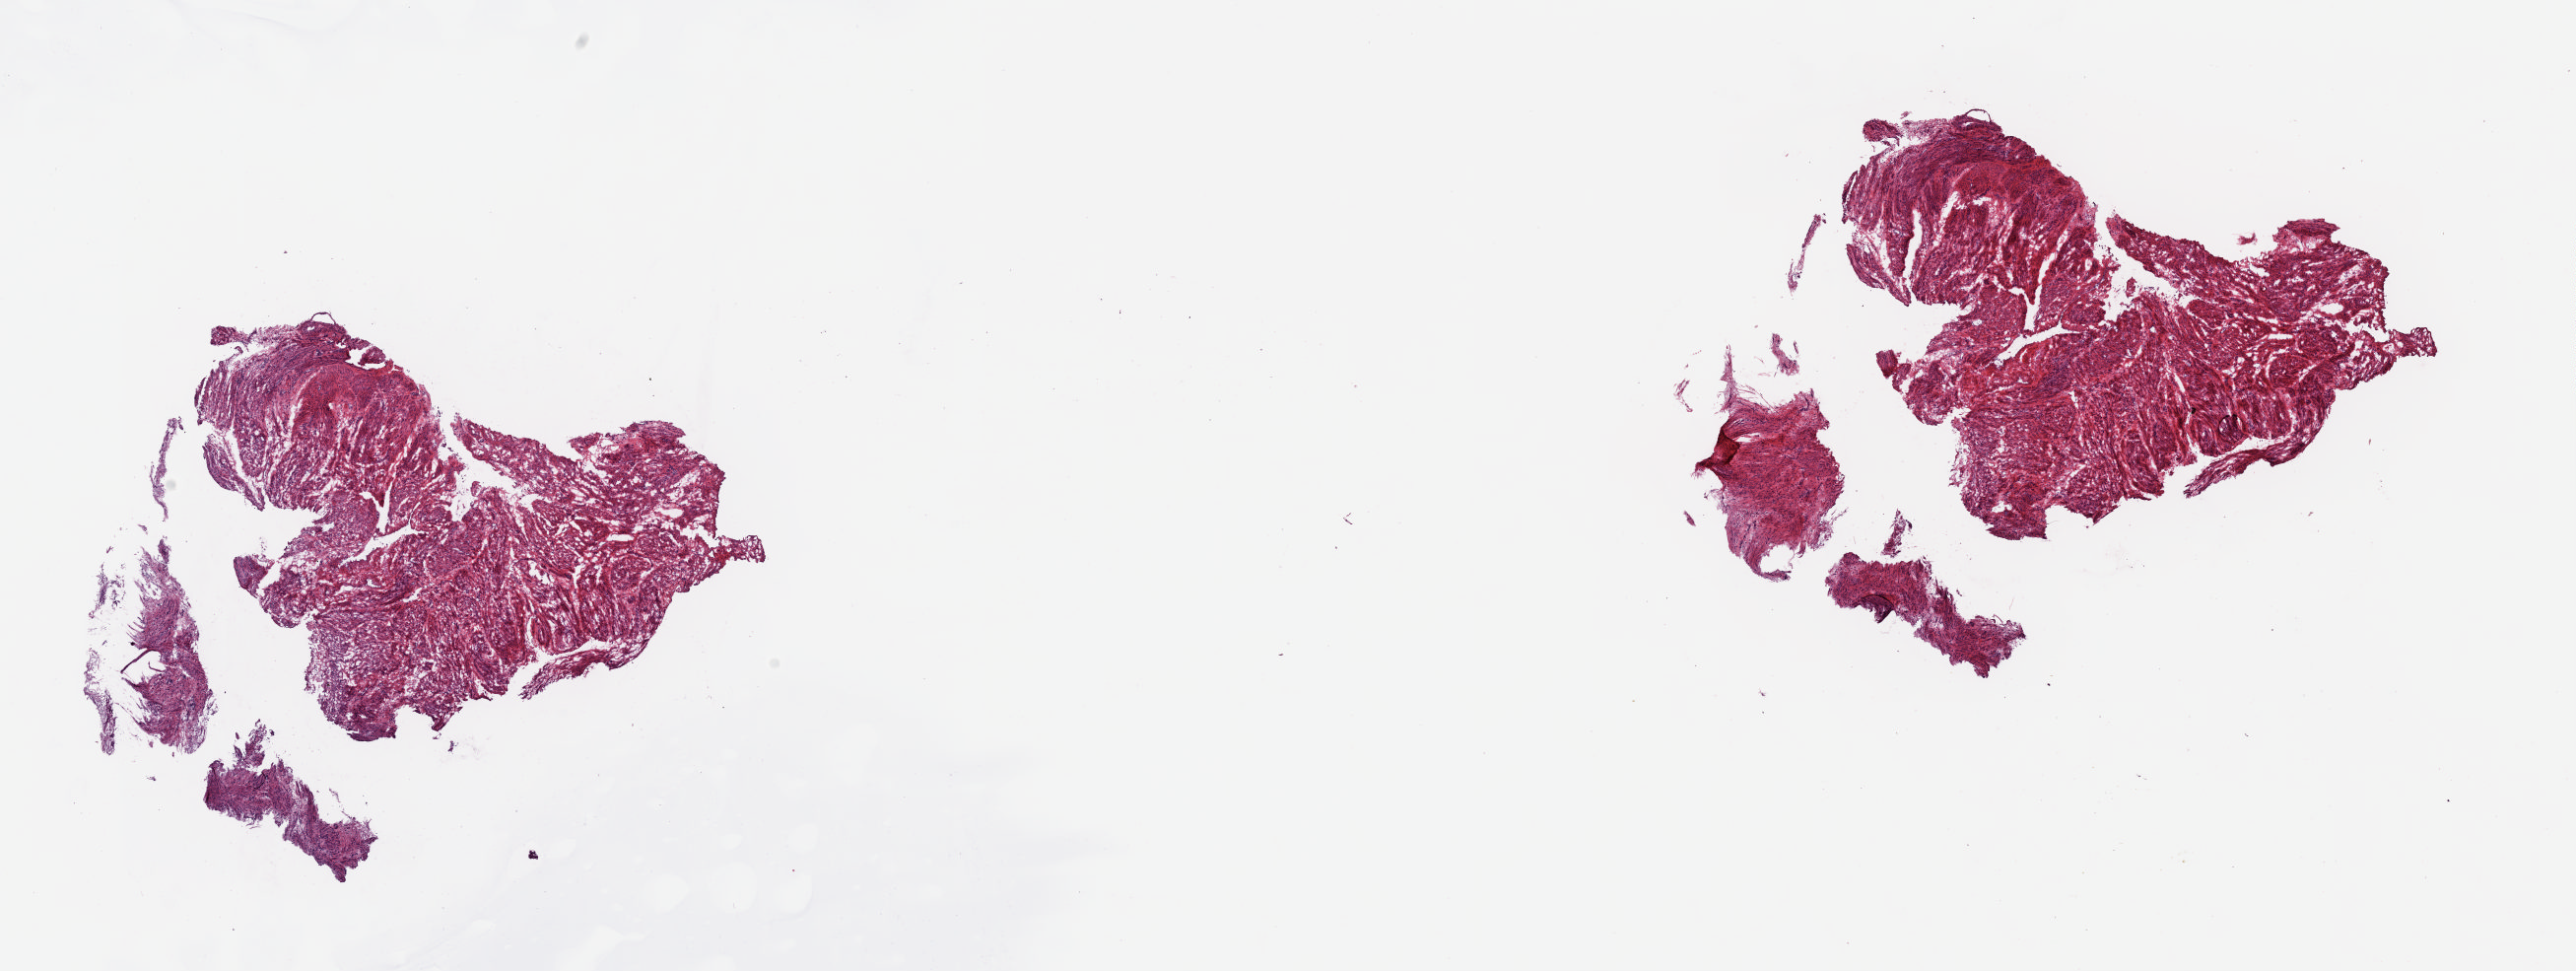
Digitized H&E tissue section (whole slide) — low-resolution overview of the scanned area, about 20.7 x 7.8 mm, frozen section, uterus, solid tissue normal (non-tumour tissue) sample. Female, age 64 years at initial diagnosis. Pathologist review of this section (percent, as recorded): tumour cells 0%, tumour nuclei 0%, normal cells 100%, stromal cells 0%, necrosis 0%. Infiltration values recorded for this section: lymphocyte infiltration 0%, monocyte infiltration 0%, neutrophil infiltration 0%.
This section: solid tissue normal sample (biorepository sample class). Patient diagnosis: Endometrioid adenocarcinoma, NOS.